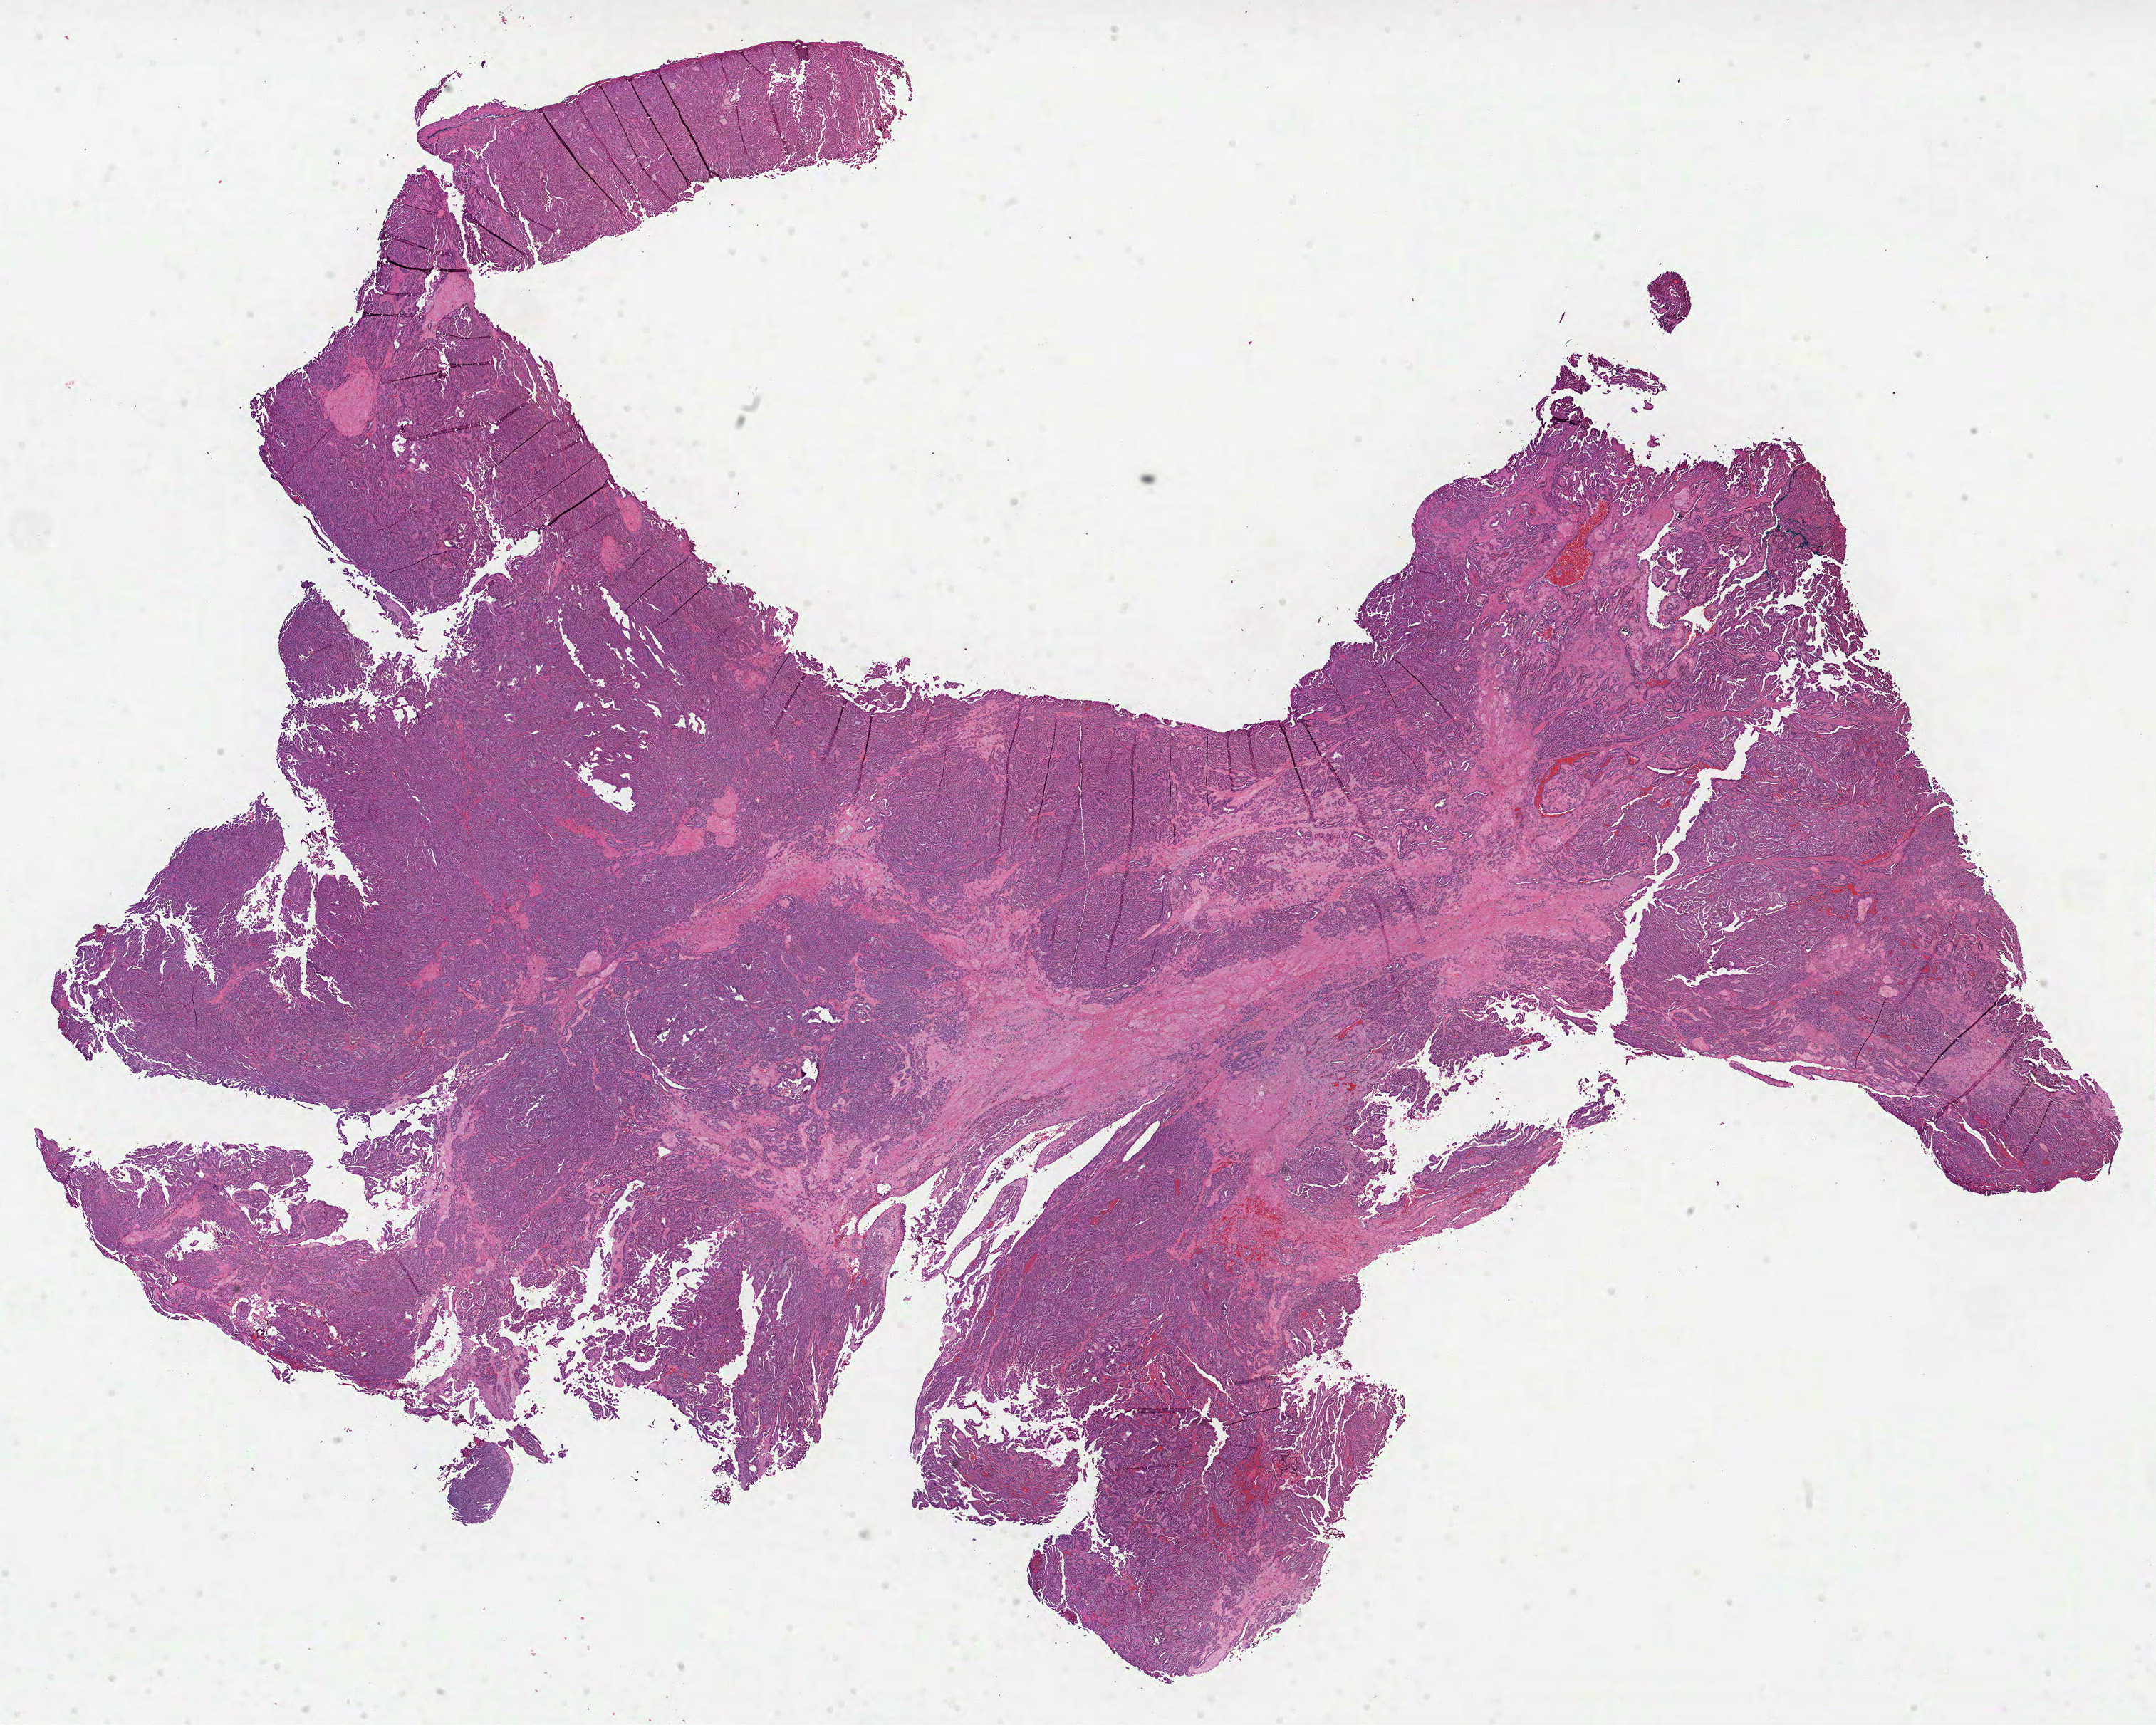
Whole-slide histology image, Hematoxylin and eosin (H&E) stained — whole scanned area (about 24.4 x 19.5 mm, slide scanned at 40x) shown as a low-resolution overview; formalin-fixed paraffin-embedded (FFPE) diagnostic section; kidney, primary tumour sample. Patient: female, age at initial diagnosis 58 years.
TNM: T1b NX MX. Laterality: right. AJCC pathologic stage: I (7th edition). Histologic diagnosis: Papillary adenocarcinoma, NOS.